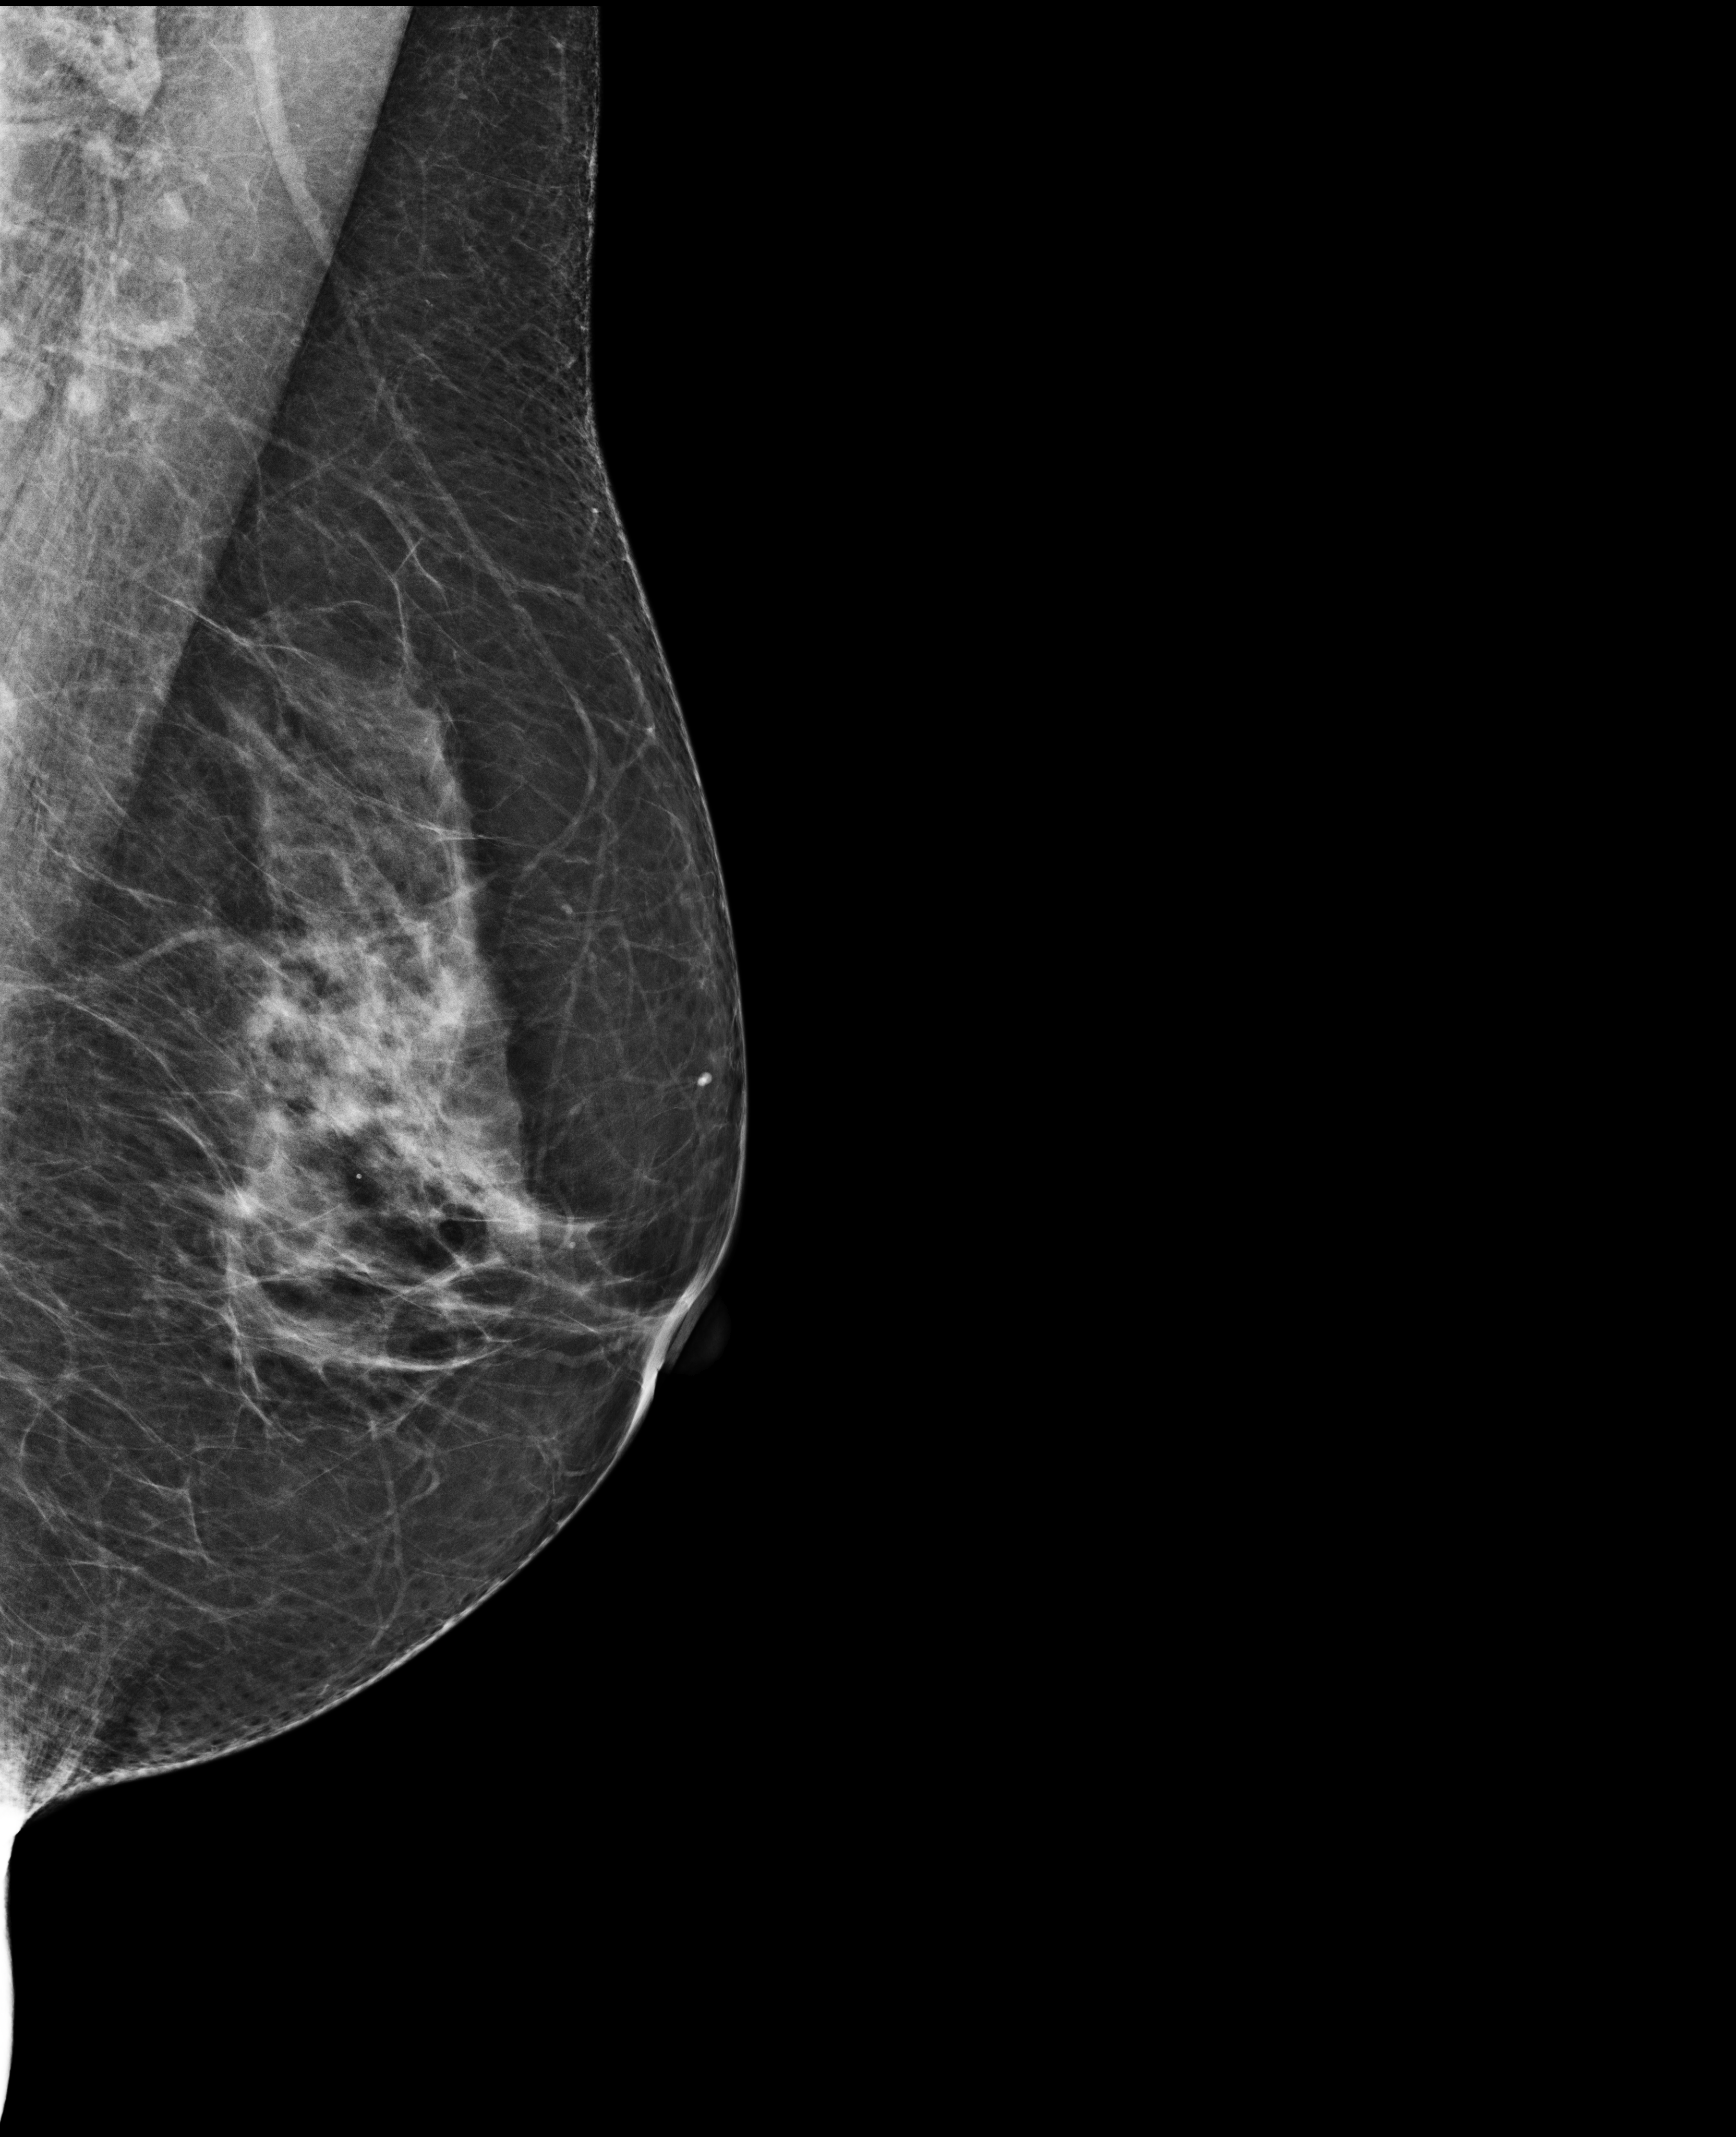
Annual screening mammography examination; compressed breast thickness 75 mm. Female patient, age 64 years.
Image type: full-field digital mammogram. Breast: left. Projection: mediolateral oblique (MLO) view.